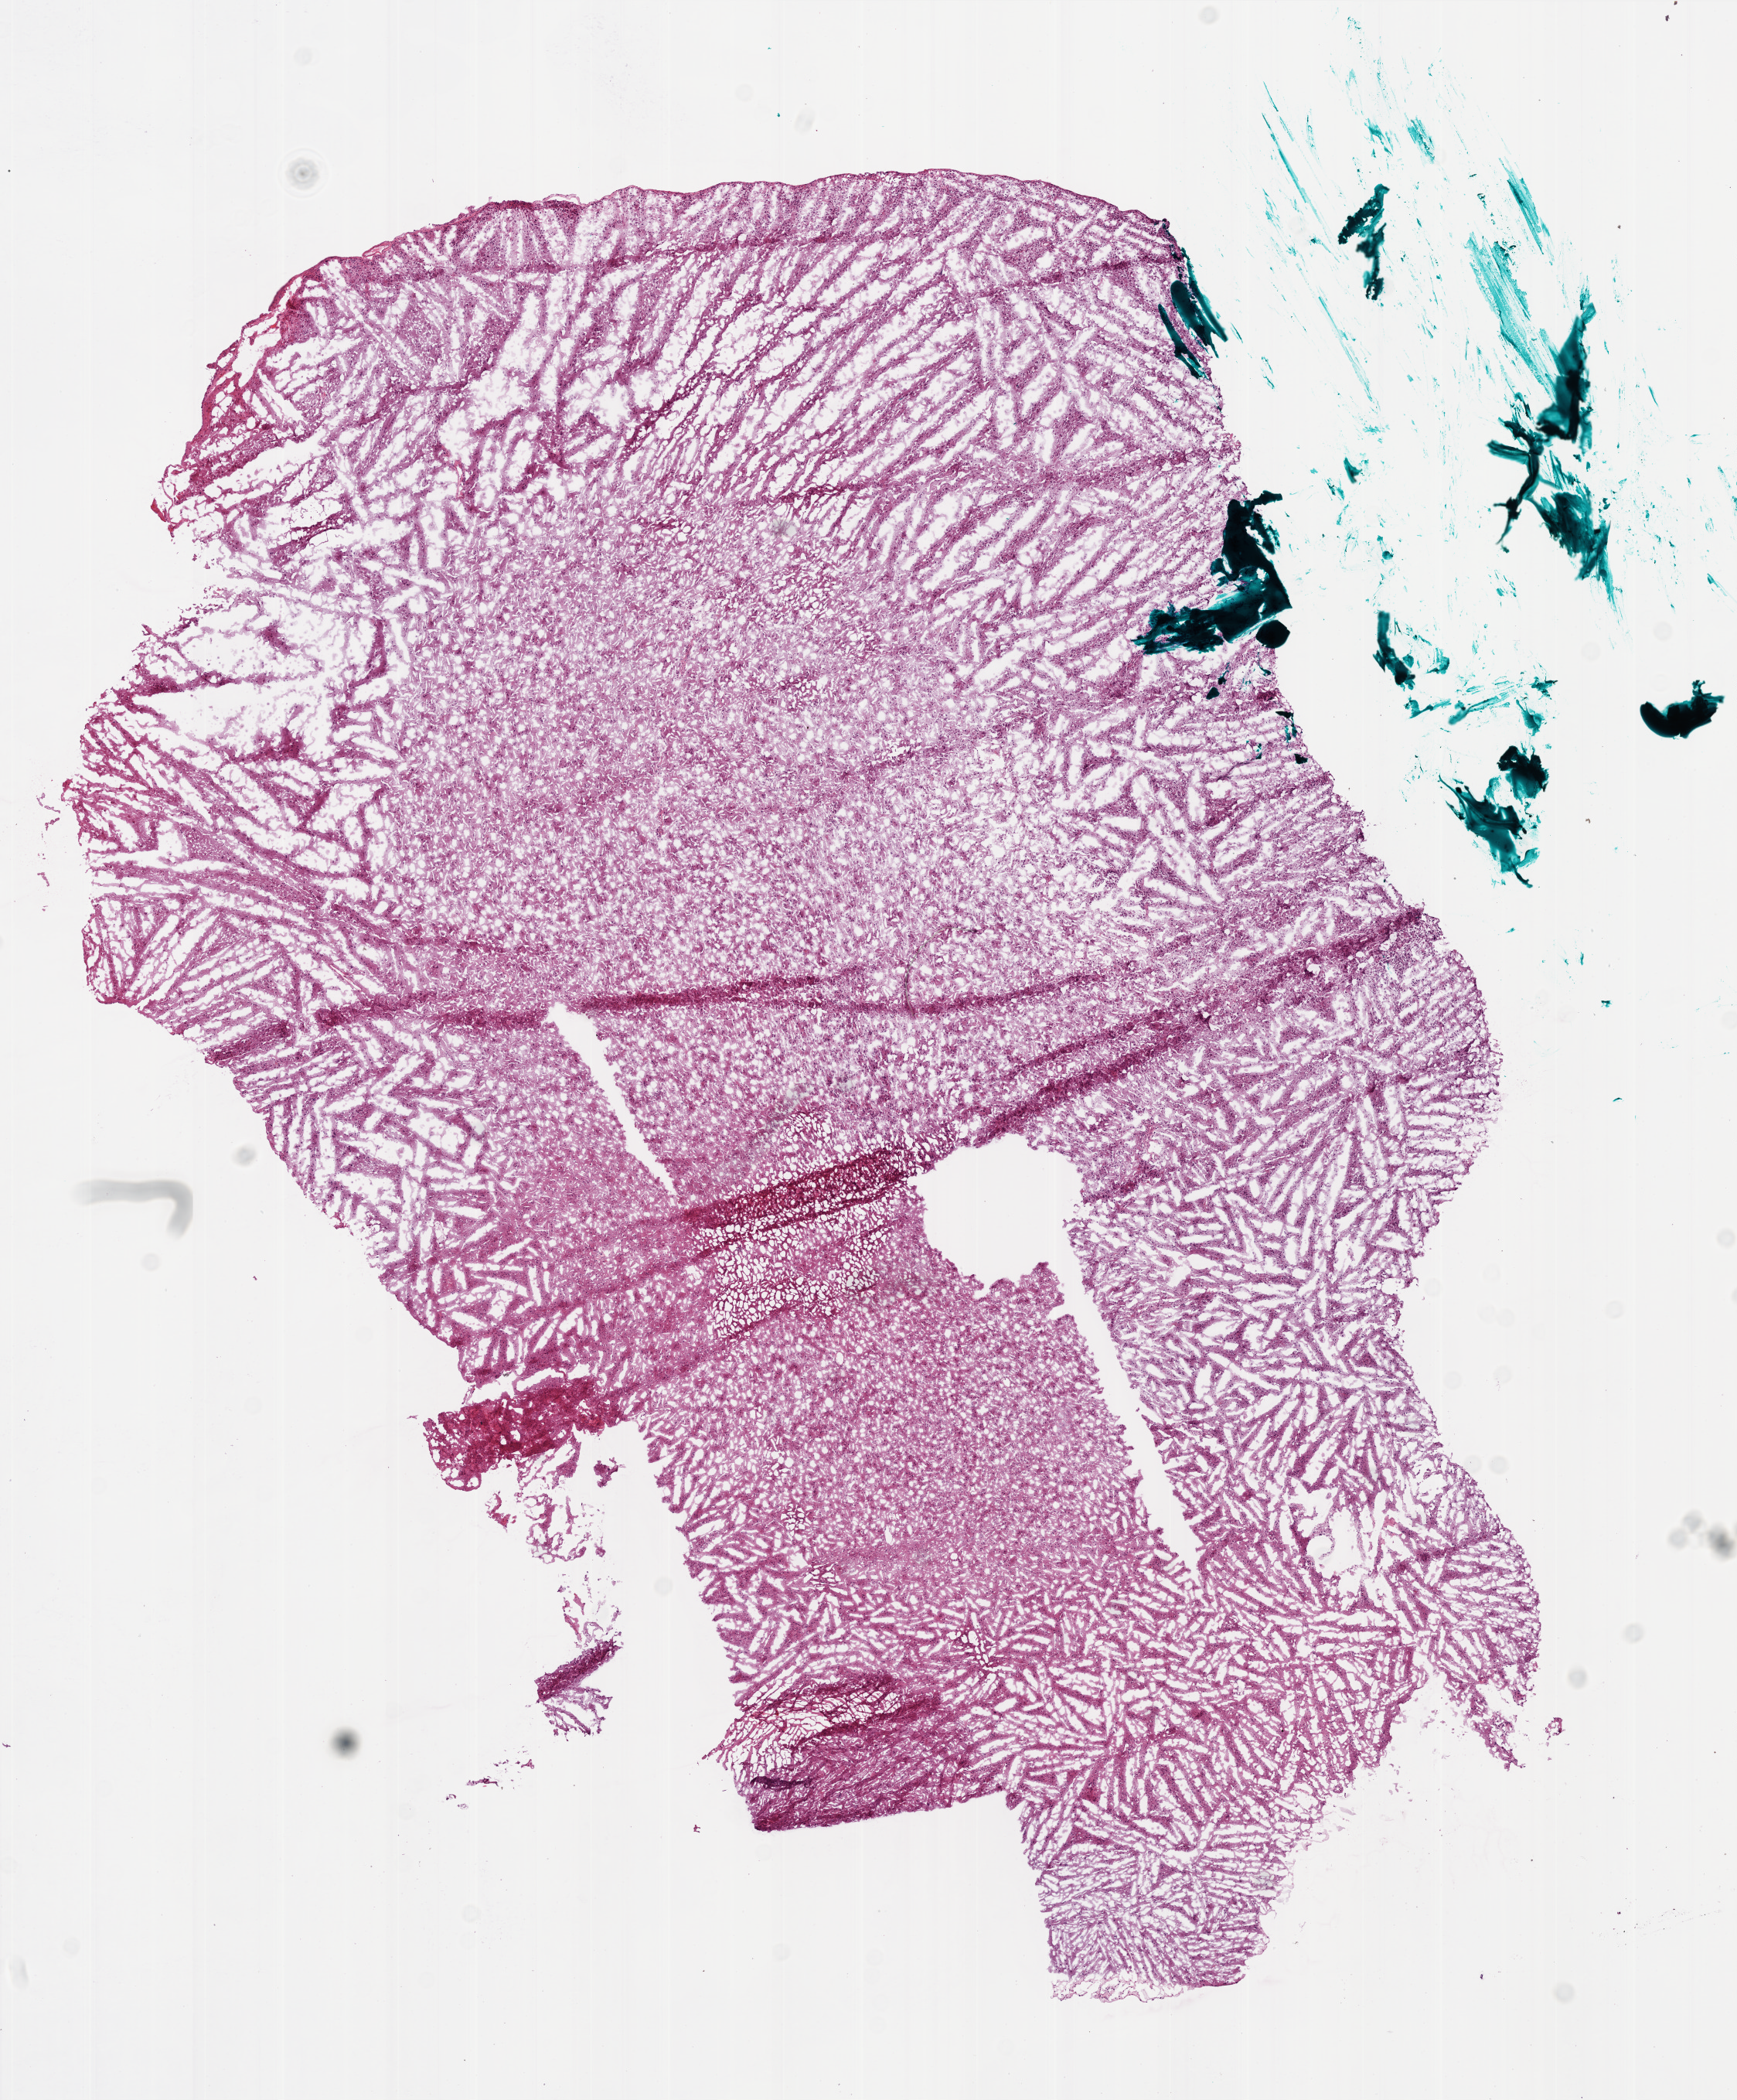
Whole-slide histology image, H&E-stained, whole scanned area (about 9.0 x 10.9 mm, acquisition: 20x scan) shown as a low-resolution overview, frozen section from the bottom of the tissue portion, sample: primary tumour, brain. Female, age 49 years at initial diagnosis. Slide review estimates, as recorded: tumour cells 95%, tumour nuclei 100%, normal cells 0%, stromal cells 0%, necrosis 5%. Infiltration values recorded for this section: lymphocyte infiltration 0%.
* pathologic diagnosis: Glioblastoma